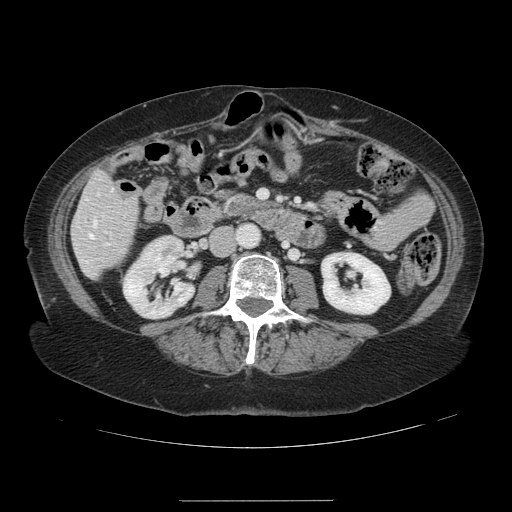
Contrast-enhanced abdominal CT, one axial slice; position 33 of 141 along the scan axis; intravenous contrast given; soft-tissue window (W 400 / L 40 HU); 2.5 mm slice thickness; 512 × 512 image matrix, field of view 393 × 393 mm. Female patient, age 74 years. From the clinical record (not read from this slice): diagnosis: colorectal cancer liver metastases, imaged before liver resection; multiple liver metastases: yes; largest metastasis: 7 cm; chemotherapy before resection: no.
Annotated regions visible in this slice (manually delineated by an expert):
- hepatic veins: bounding box <90,218,96,237> (left, top, right, bottom; pixels)
- liver: <72,173,139,278>
- planned liver remnant (the part of the liver to remain after resection): <77,173,132,278>